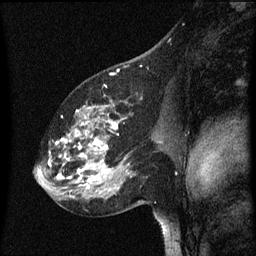
Breast MRI (dynamic contrast-enhanced), one sagittal slice. Dynamic contrast-enhanced series, image 2 of 3 at this slice position (ordered by acquisition). 1.5 T. TE 4.2 ms, TR 8 ms. 2 mm slice thickness. 256 × 256 image matrix, field of view 200 × 200 mm. Patient: female, 60 years.
Outlined on this slice (semi-automatic segmentation, software-assisted and operator-edited):
- analysis volume of interest (the breast-tissue region the enhancement analysis was run in; not a lesion): box from (x=49, y=102) to (x=158, y=197) px
- tumour enhancement mask (voxels above the 70 % enhancement threshold inside the analysis volume of interest): (x=52, y=106)–(x=119, y=189)